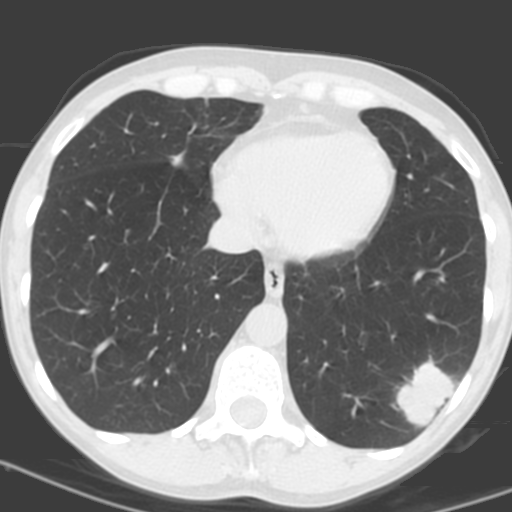
Low-dose screening chest CT, one axial slice; position 48 of 156 along the scan axis; lung window (W 1500 / L -600 HU); 3.2 mm slice thickness; 512 × 512 image matrix, field of view 262 × 262 mm.
Annotated regions visible in this slice (outlined manually by an expert reader):
- lesion 1 (tumor, lower lobe of left lung): box from (x=396, y=361) to (x=454, y=424) px